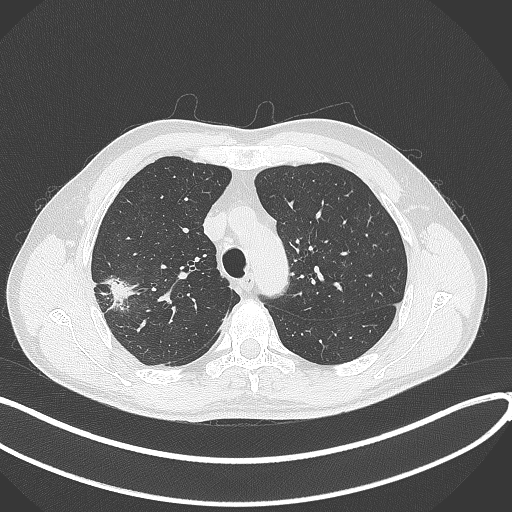
Chest CT, one axial slice; position 313 of 381 along the scan axis; reconstruction kernel B70f; 120 kVp; lung window (W 1500 / L -600 HU); 512 × 512 image matrix. Patient: male, 62 years. Case-level facts recorded for this patient, not image findings: clinical TNM (as recorded): T1c N0 M0.
Structures marked on this image (rectangle marked by the reading radiologist):
- lung tumour (recorded histology: adenocarcinoma): bounding box (x1, y1, x2, y2) in pixels: (98, 268, 142, 313)